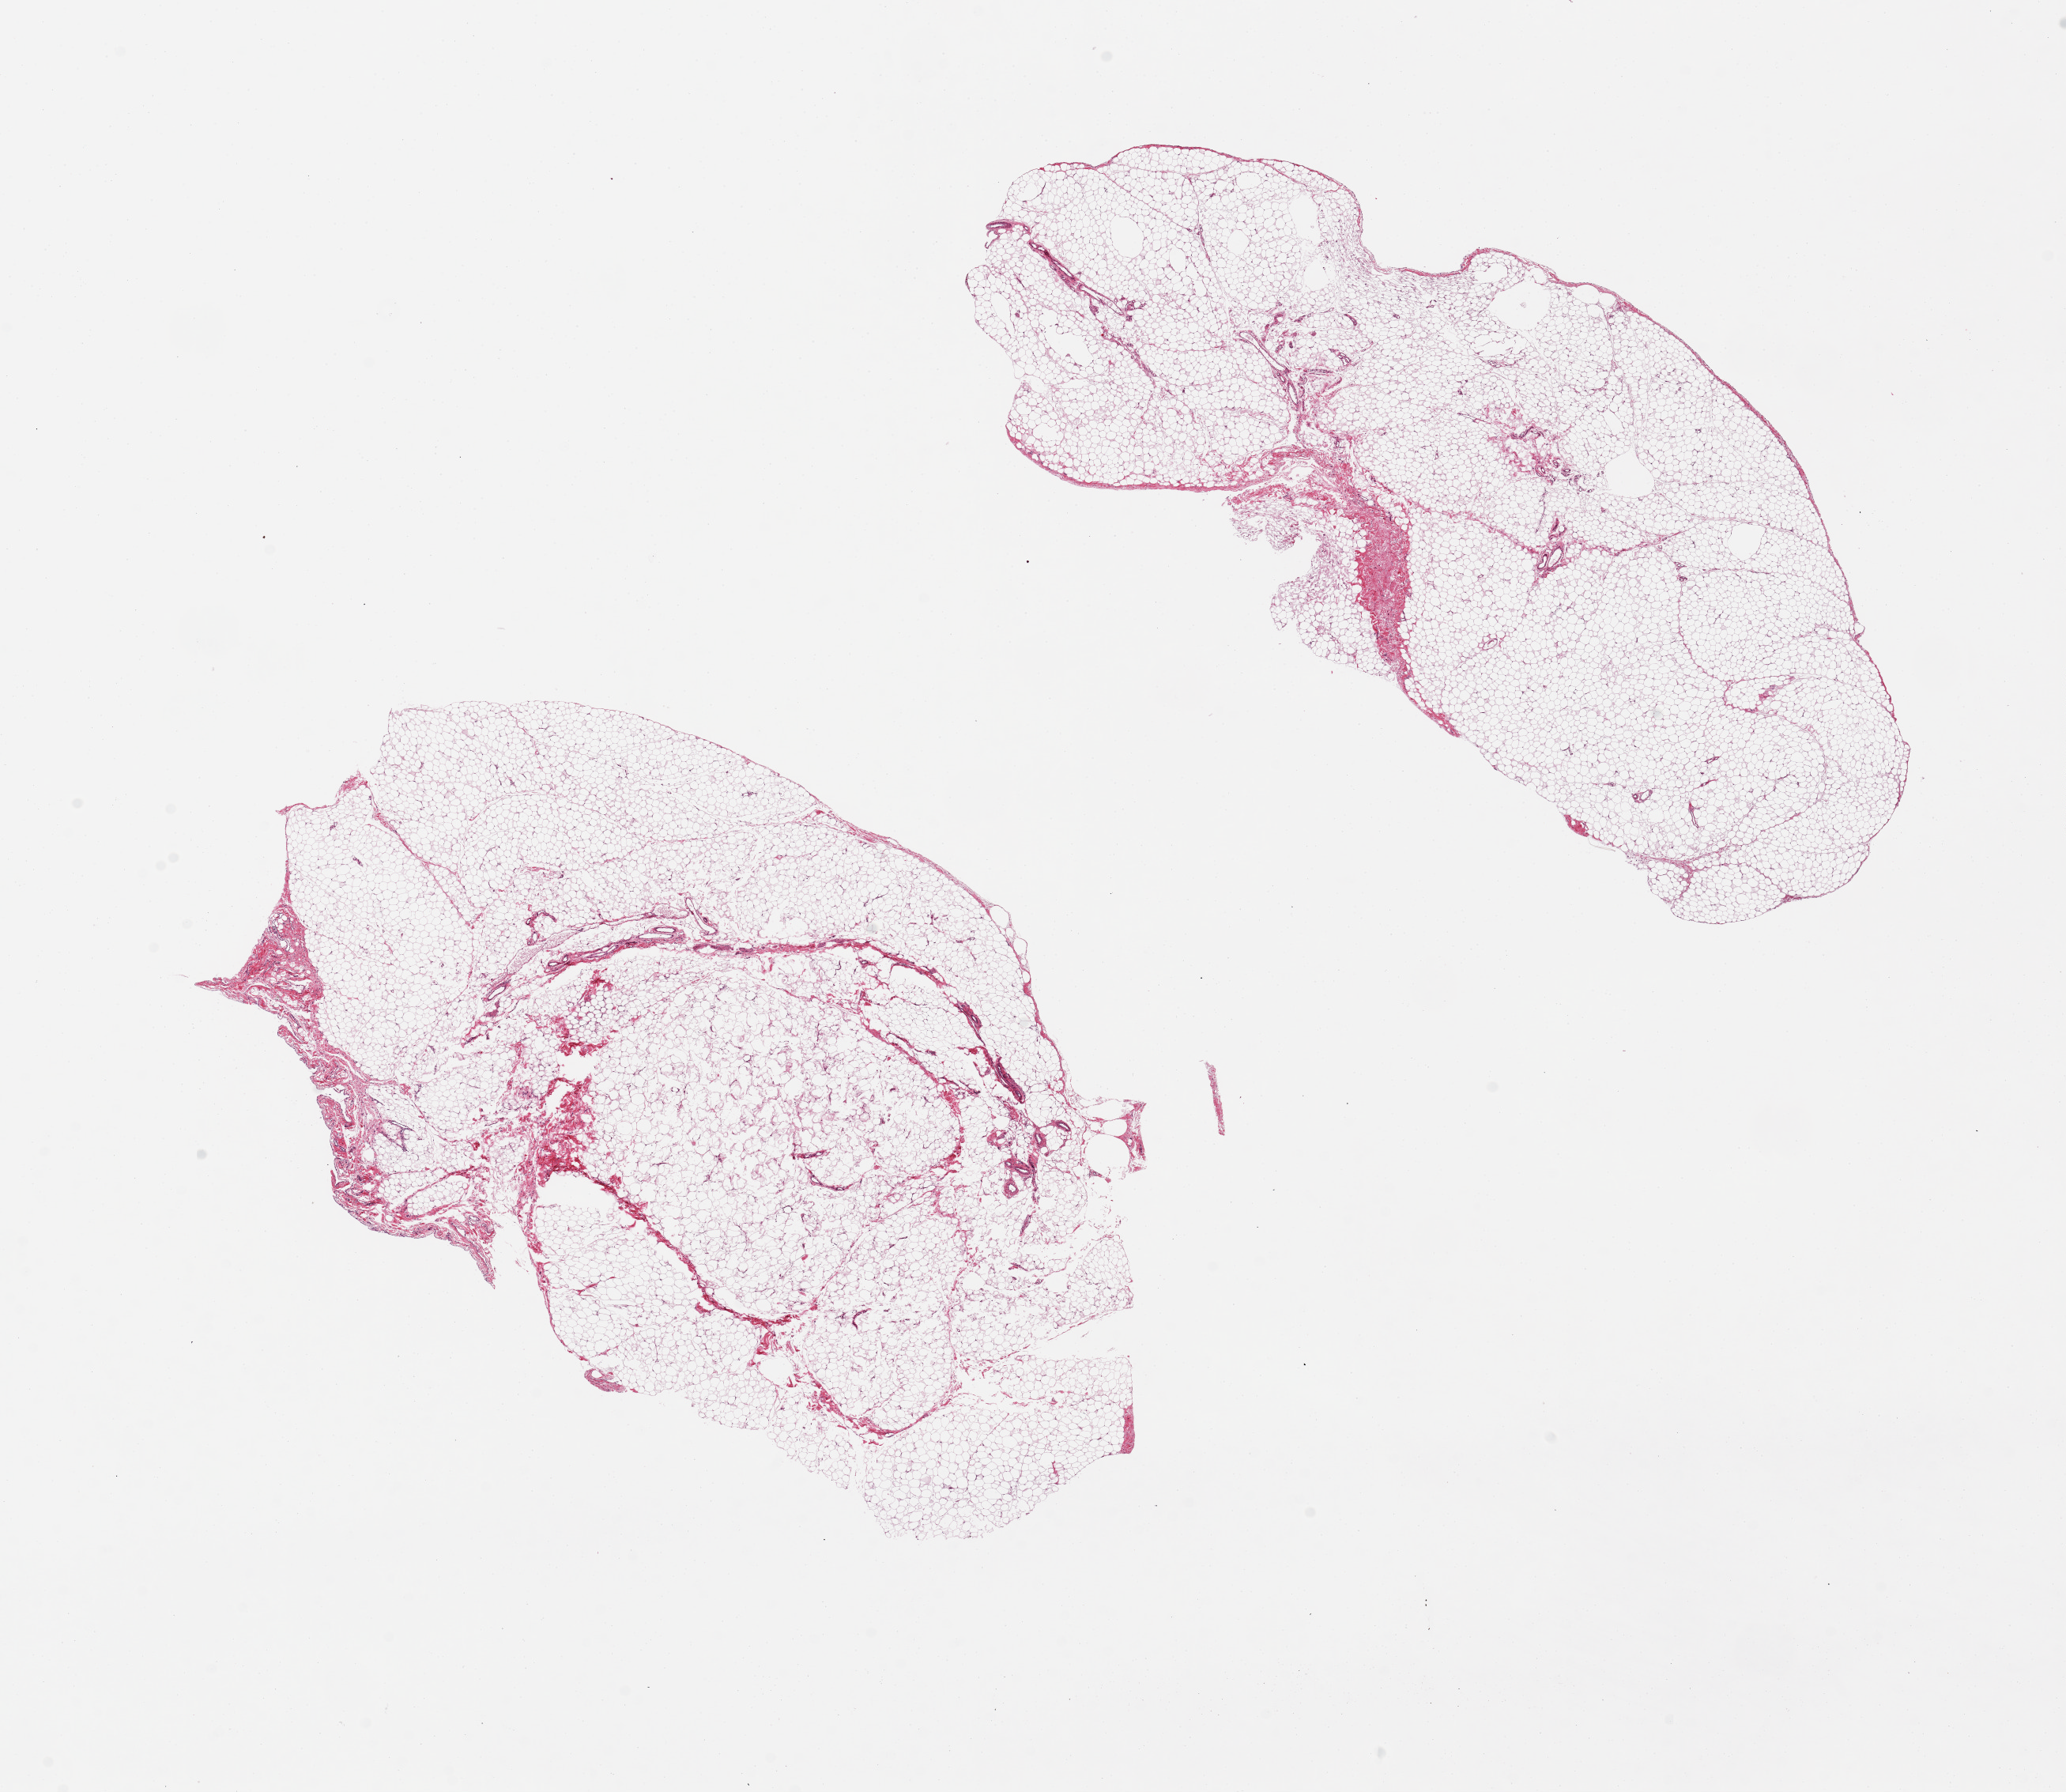
Whole-slide image, haematoxylin and eosin stain — low-resolution overview of the scanned area, about 20.7 x 17.9 mm; PAXgene-fixed paraffin-embedded (PFPE) section; section of omentum (target tissue); donor tissue sample. Donor: female.
Reviewer comment on this tissue sample: 2 pieces, 11x7 & 11x5mm; ~<5% fibrous areas.